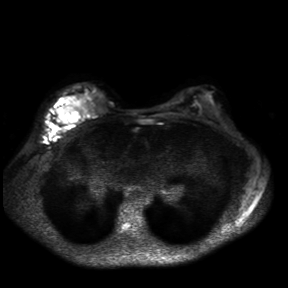
Breast MRI, one axial slice; slice 22 of 30 in the series (ordered by position); diffusion-weighted series; image 2 of 4 stored at this slice position (different b-values; order by instance number); 3 T; 4 mm slice thickness; 288 × 288 image matrix, field of view 360 × 360 mm. Female patient.
Annotated regions visible in this slice (expert manual segmentation):
- tumour on diffusion-weighted imaging: bounding box [x1, y1, x2, y2] px = [57, 97, 70, 123]